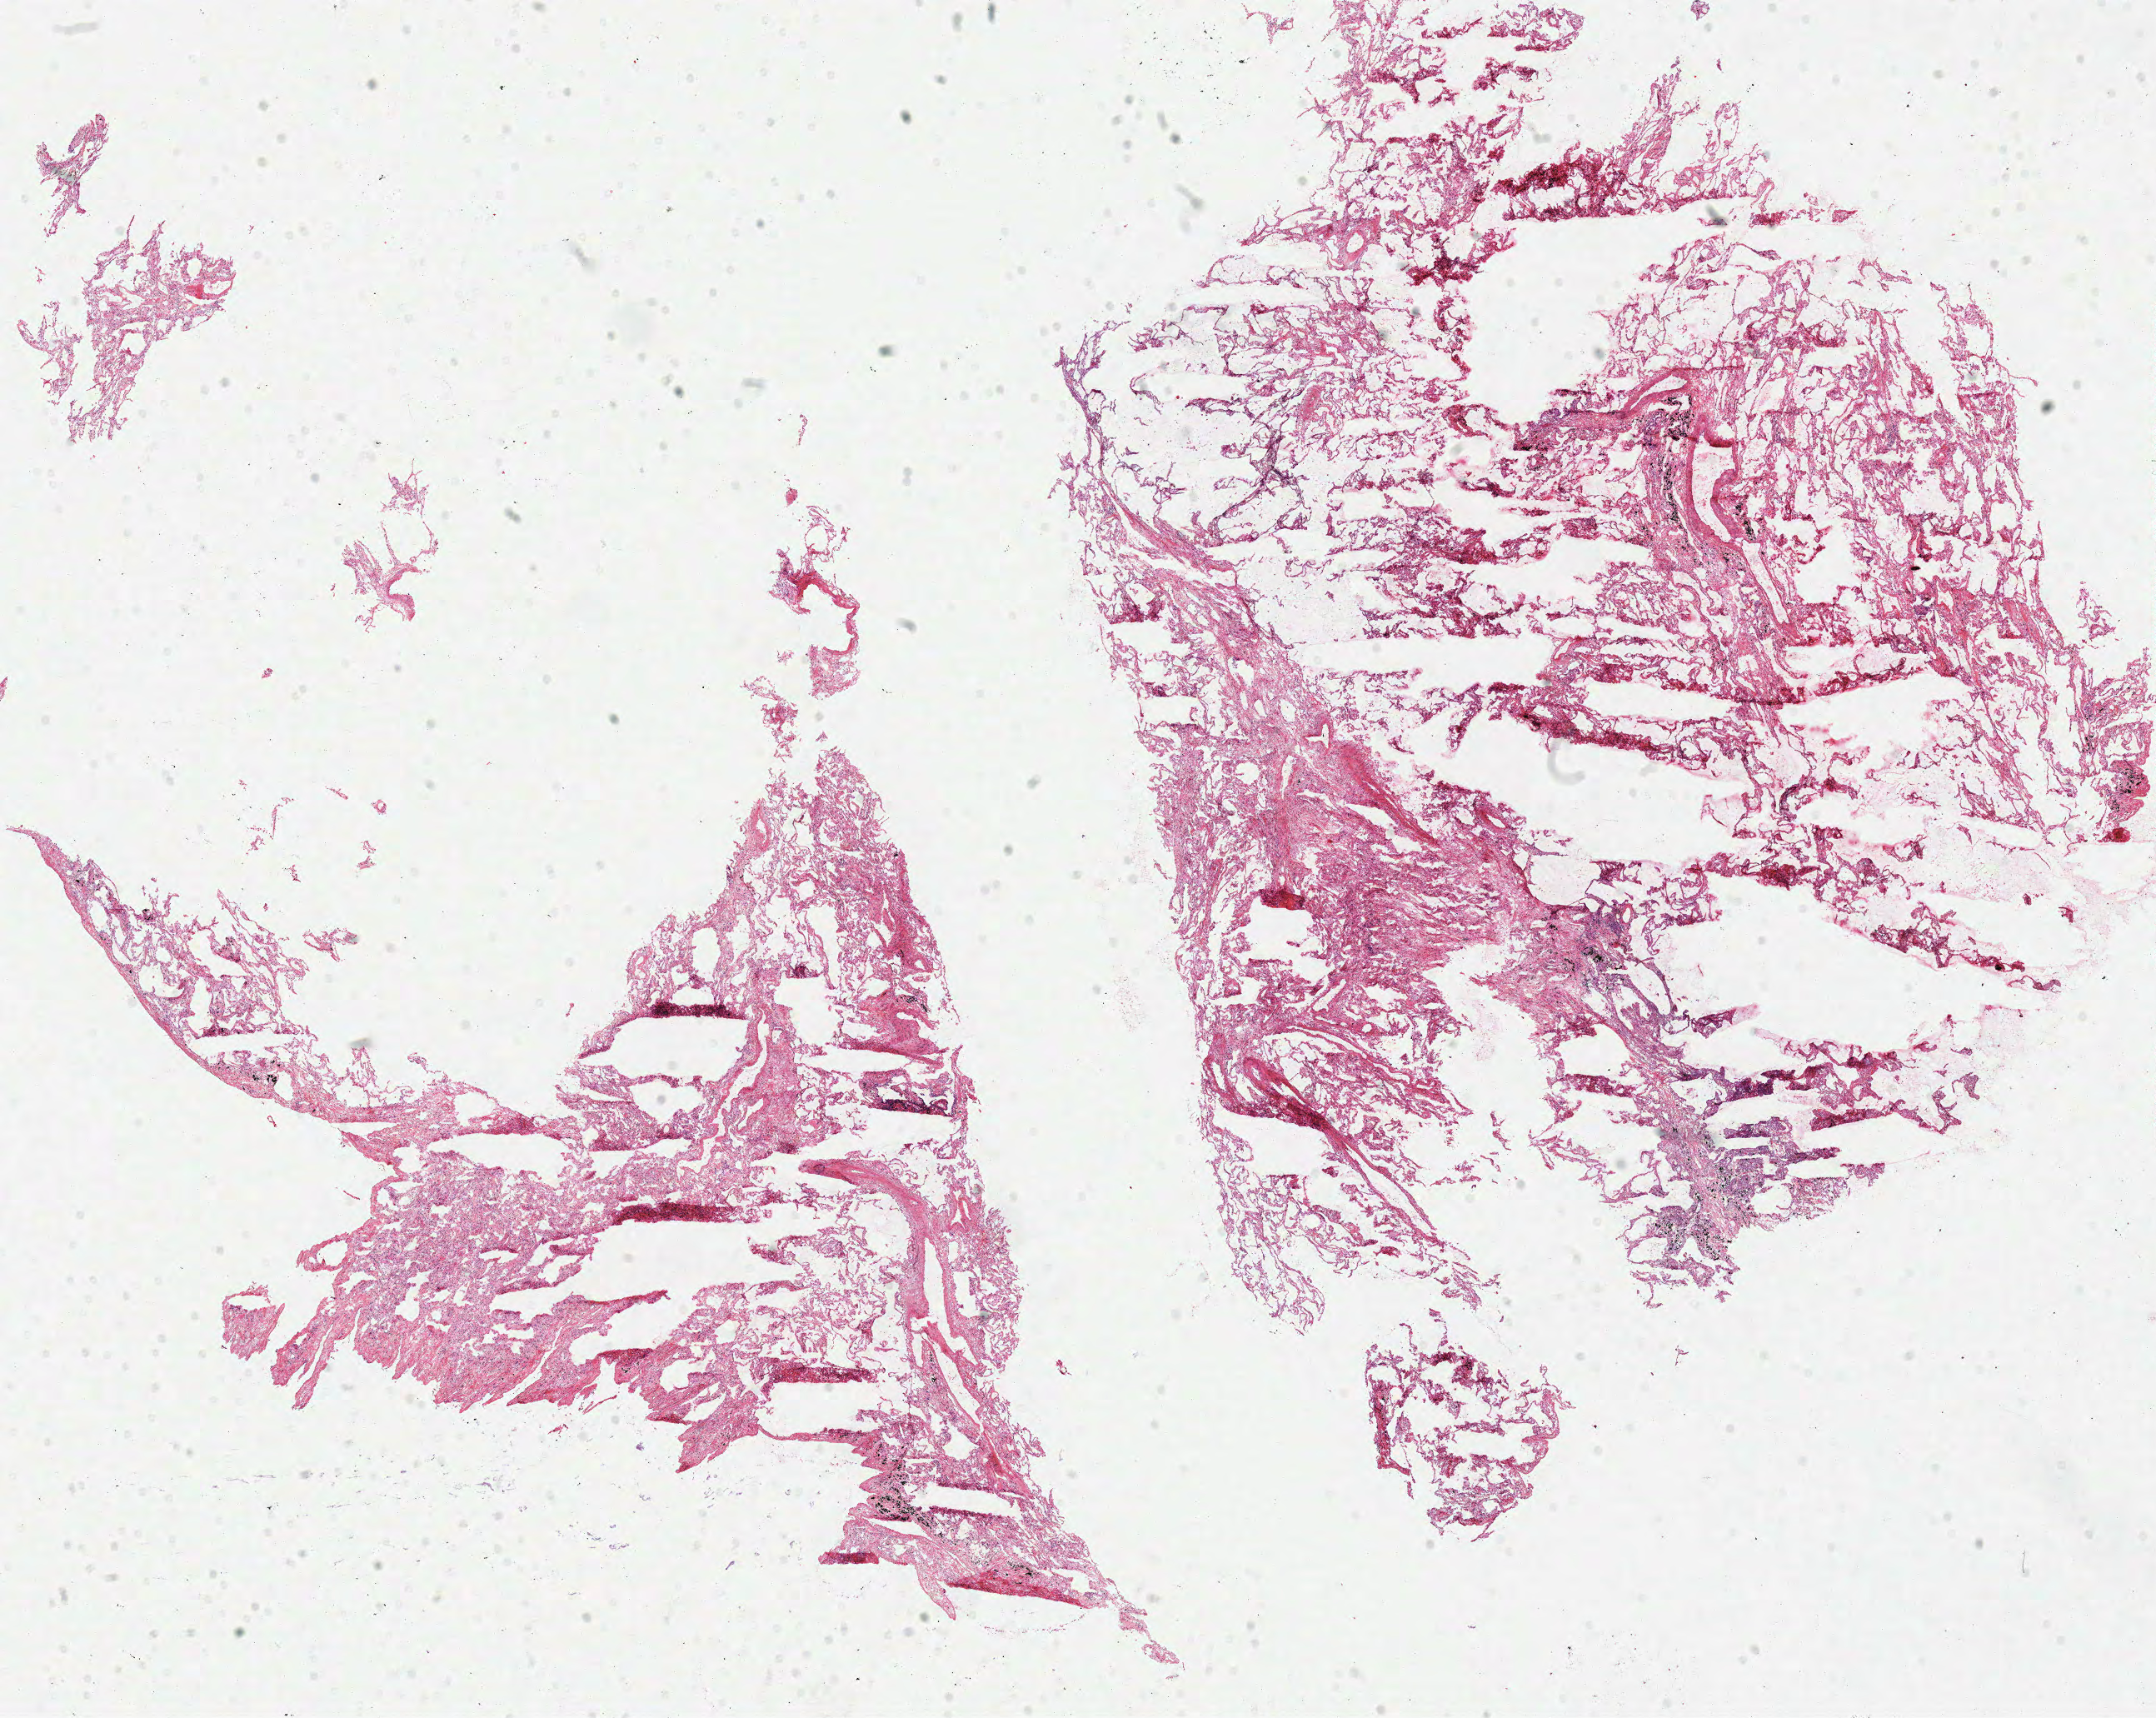
Whole-slide histology image, Hematoxylin and eosin (H&E) stained, shown as a low-resolution overview of the whole scanned area (about 20.4 x 16.2 mm). Frozen section. Solid tissue normal (non-tumour tissue) sample from the lung. Female patient; age at initial diagnosis 74 years.
This section: solid tissue normal (non-tumour) sample from the same patient. Patient diagnosis: Adenocarcinoma, NOS (upper lobe, lung).